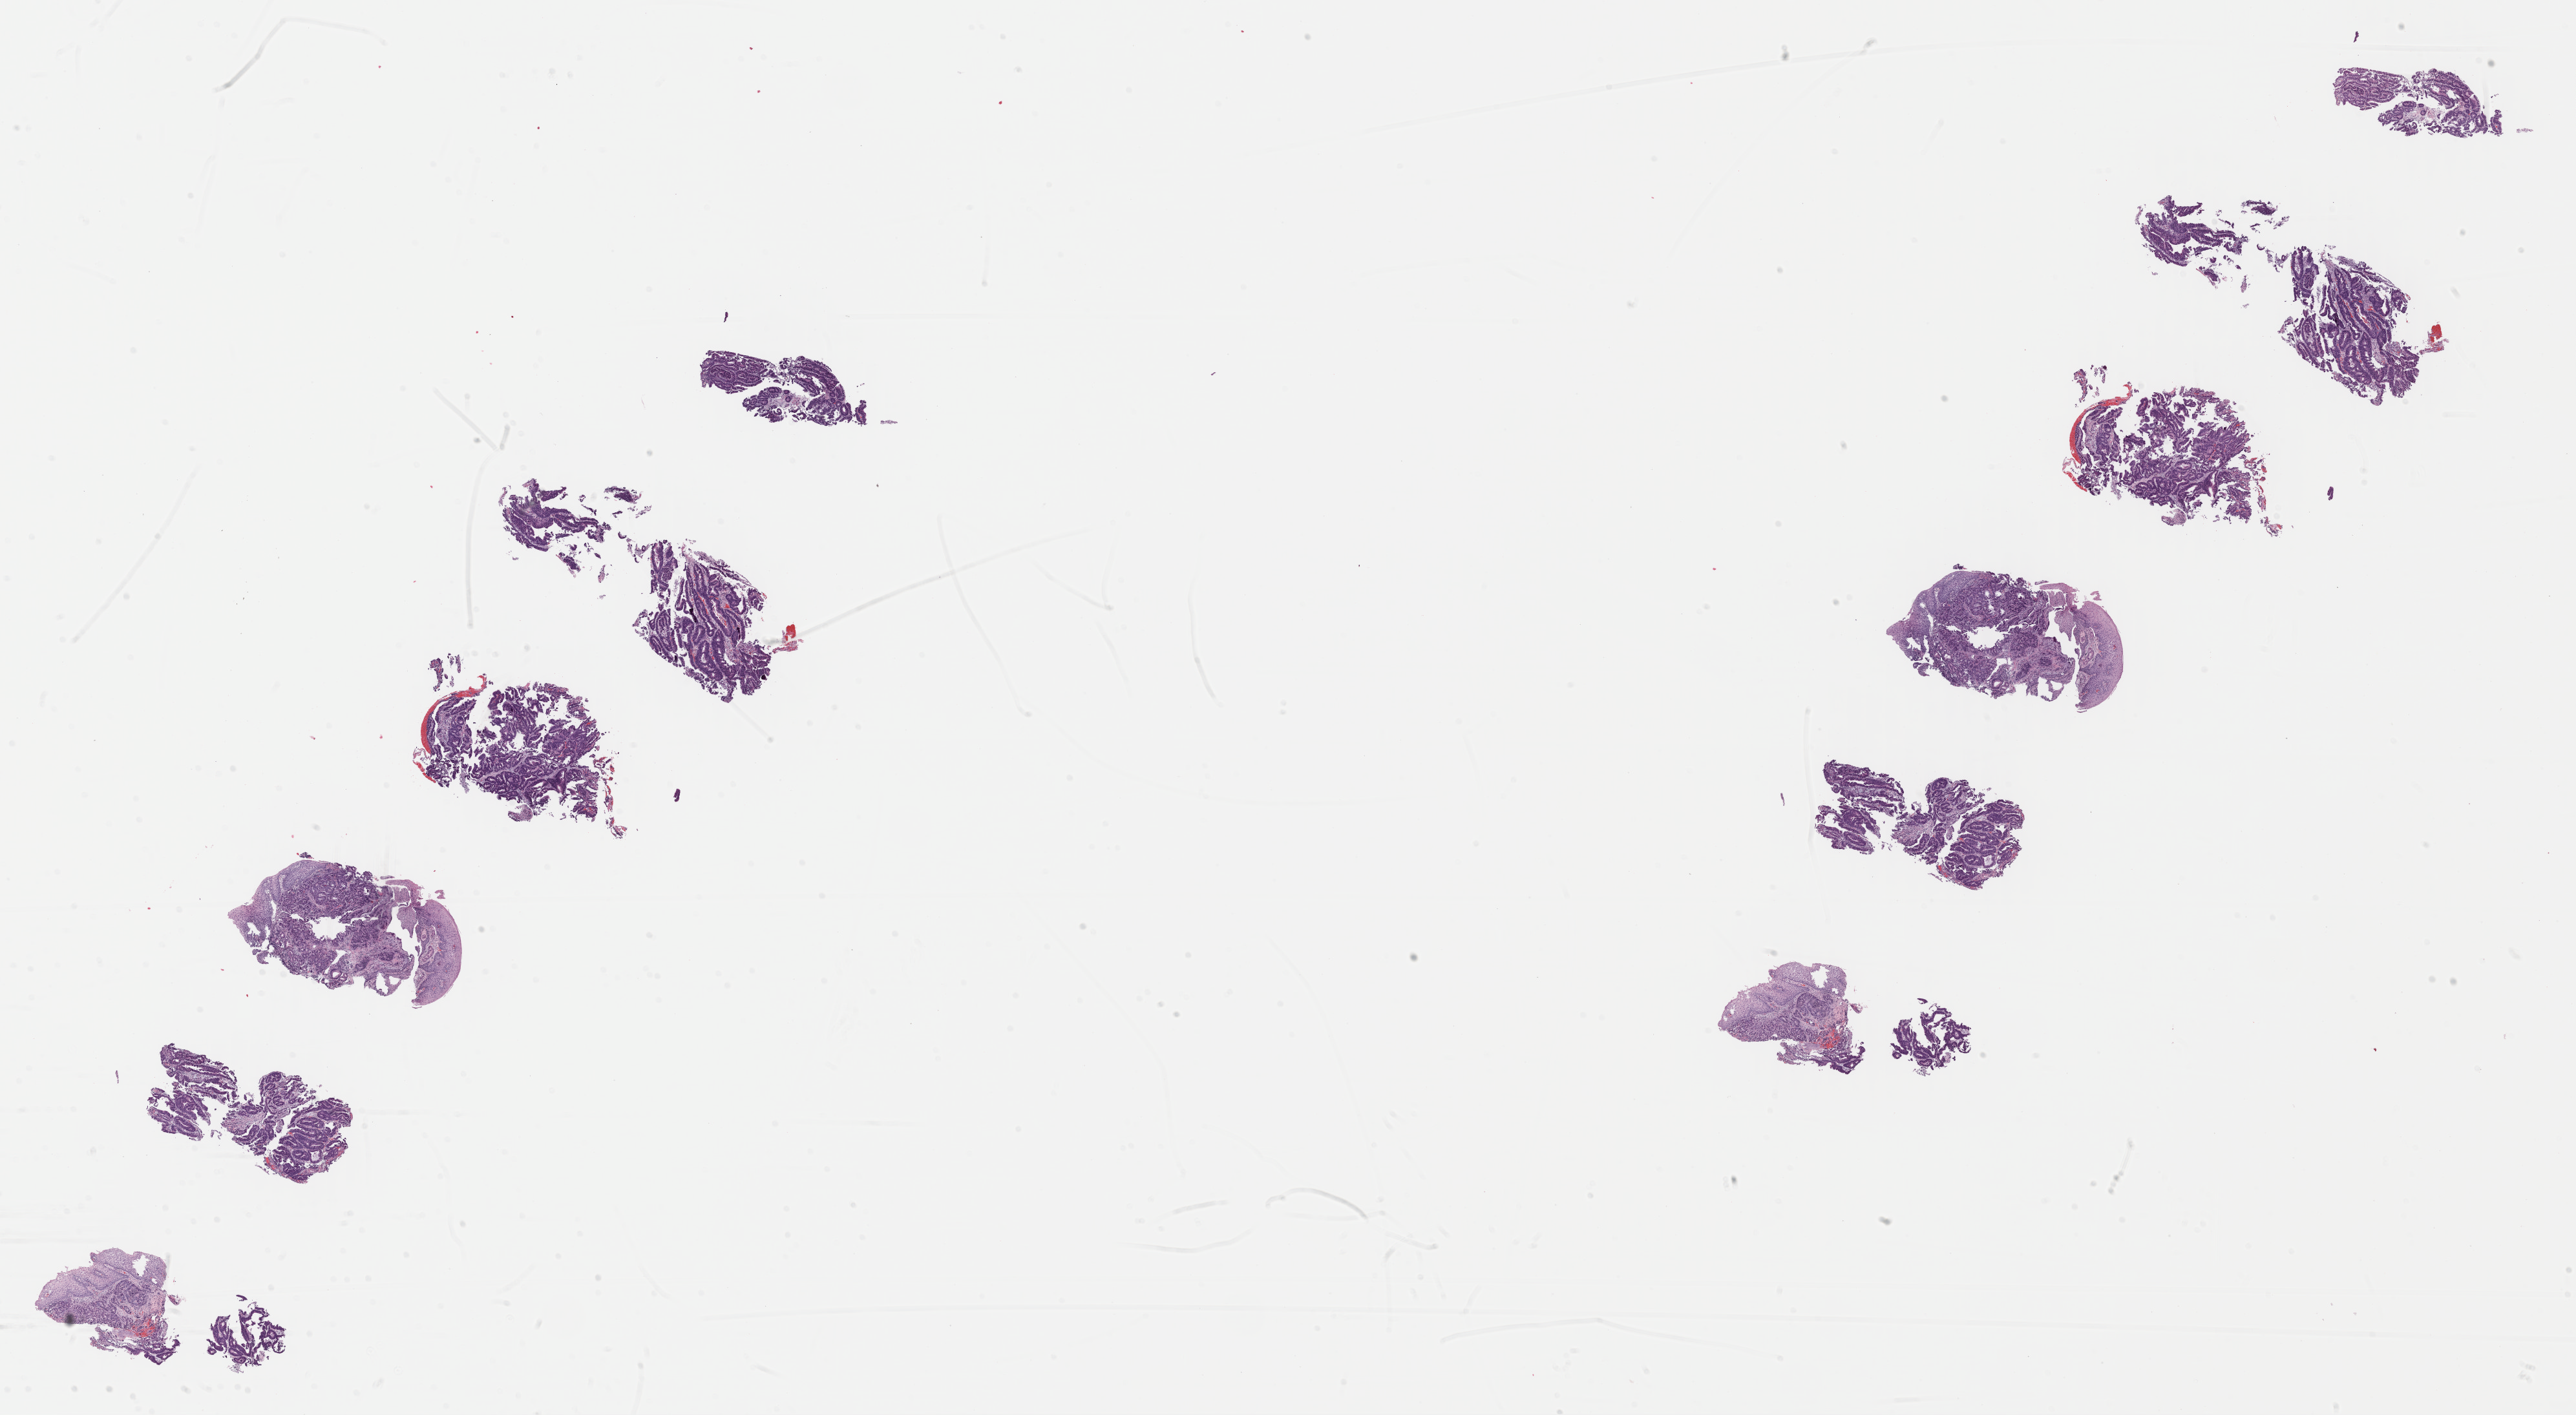
Whole-slide histology image, Hematoxylin and eosin (H&E) stained — a low-resolution overview of the entire scanned area, about 31.3 x 17.2 mm (slide scanned at 40x), FFPE section, primary tumour sample from the esophagus. Patient: male, age at initial diagnosis 27 years. Histologic grade: G2 (moderately differentiated). Slide review estimates, as recorded: tumour cells 50%, tumour nuclei 60%, normal cells 30%, stromal cells 20%, necrosis 0%. Infiltration values recorded for this section: lymphocyte infiltration 0%, monocyte infiltration 0%, neutrophil infiltration 0%.
Diagnosis: Adenocarcinoma, NOS.